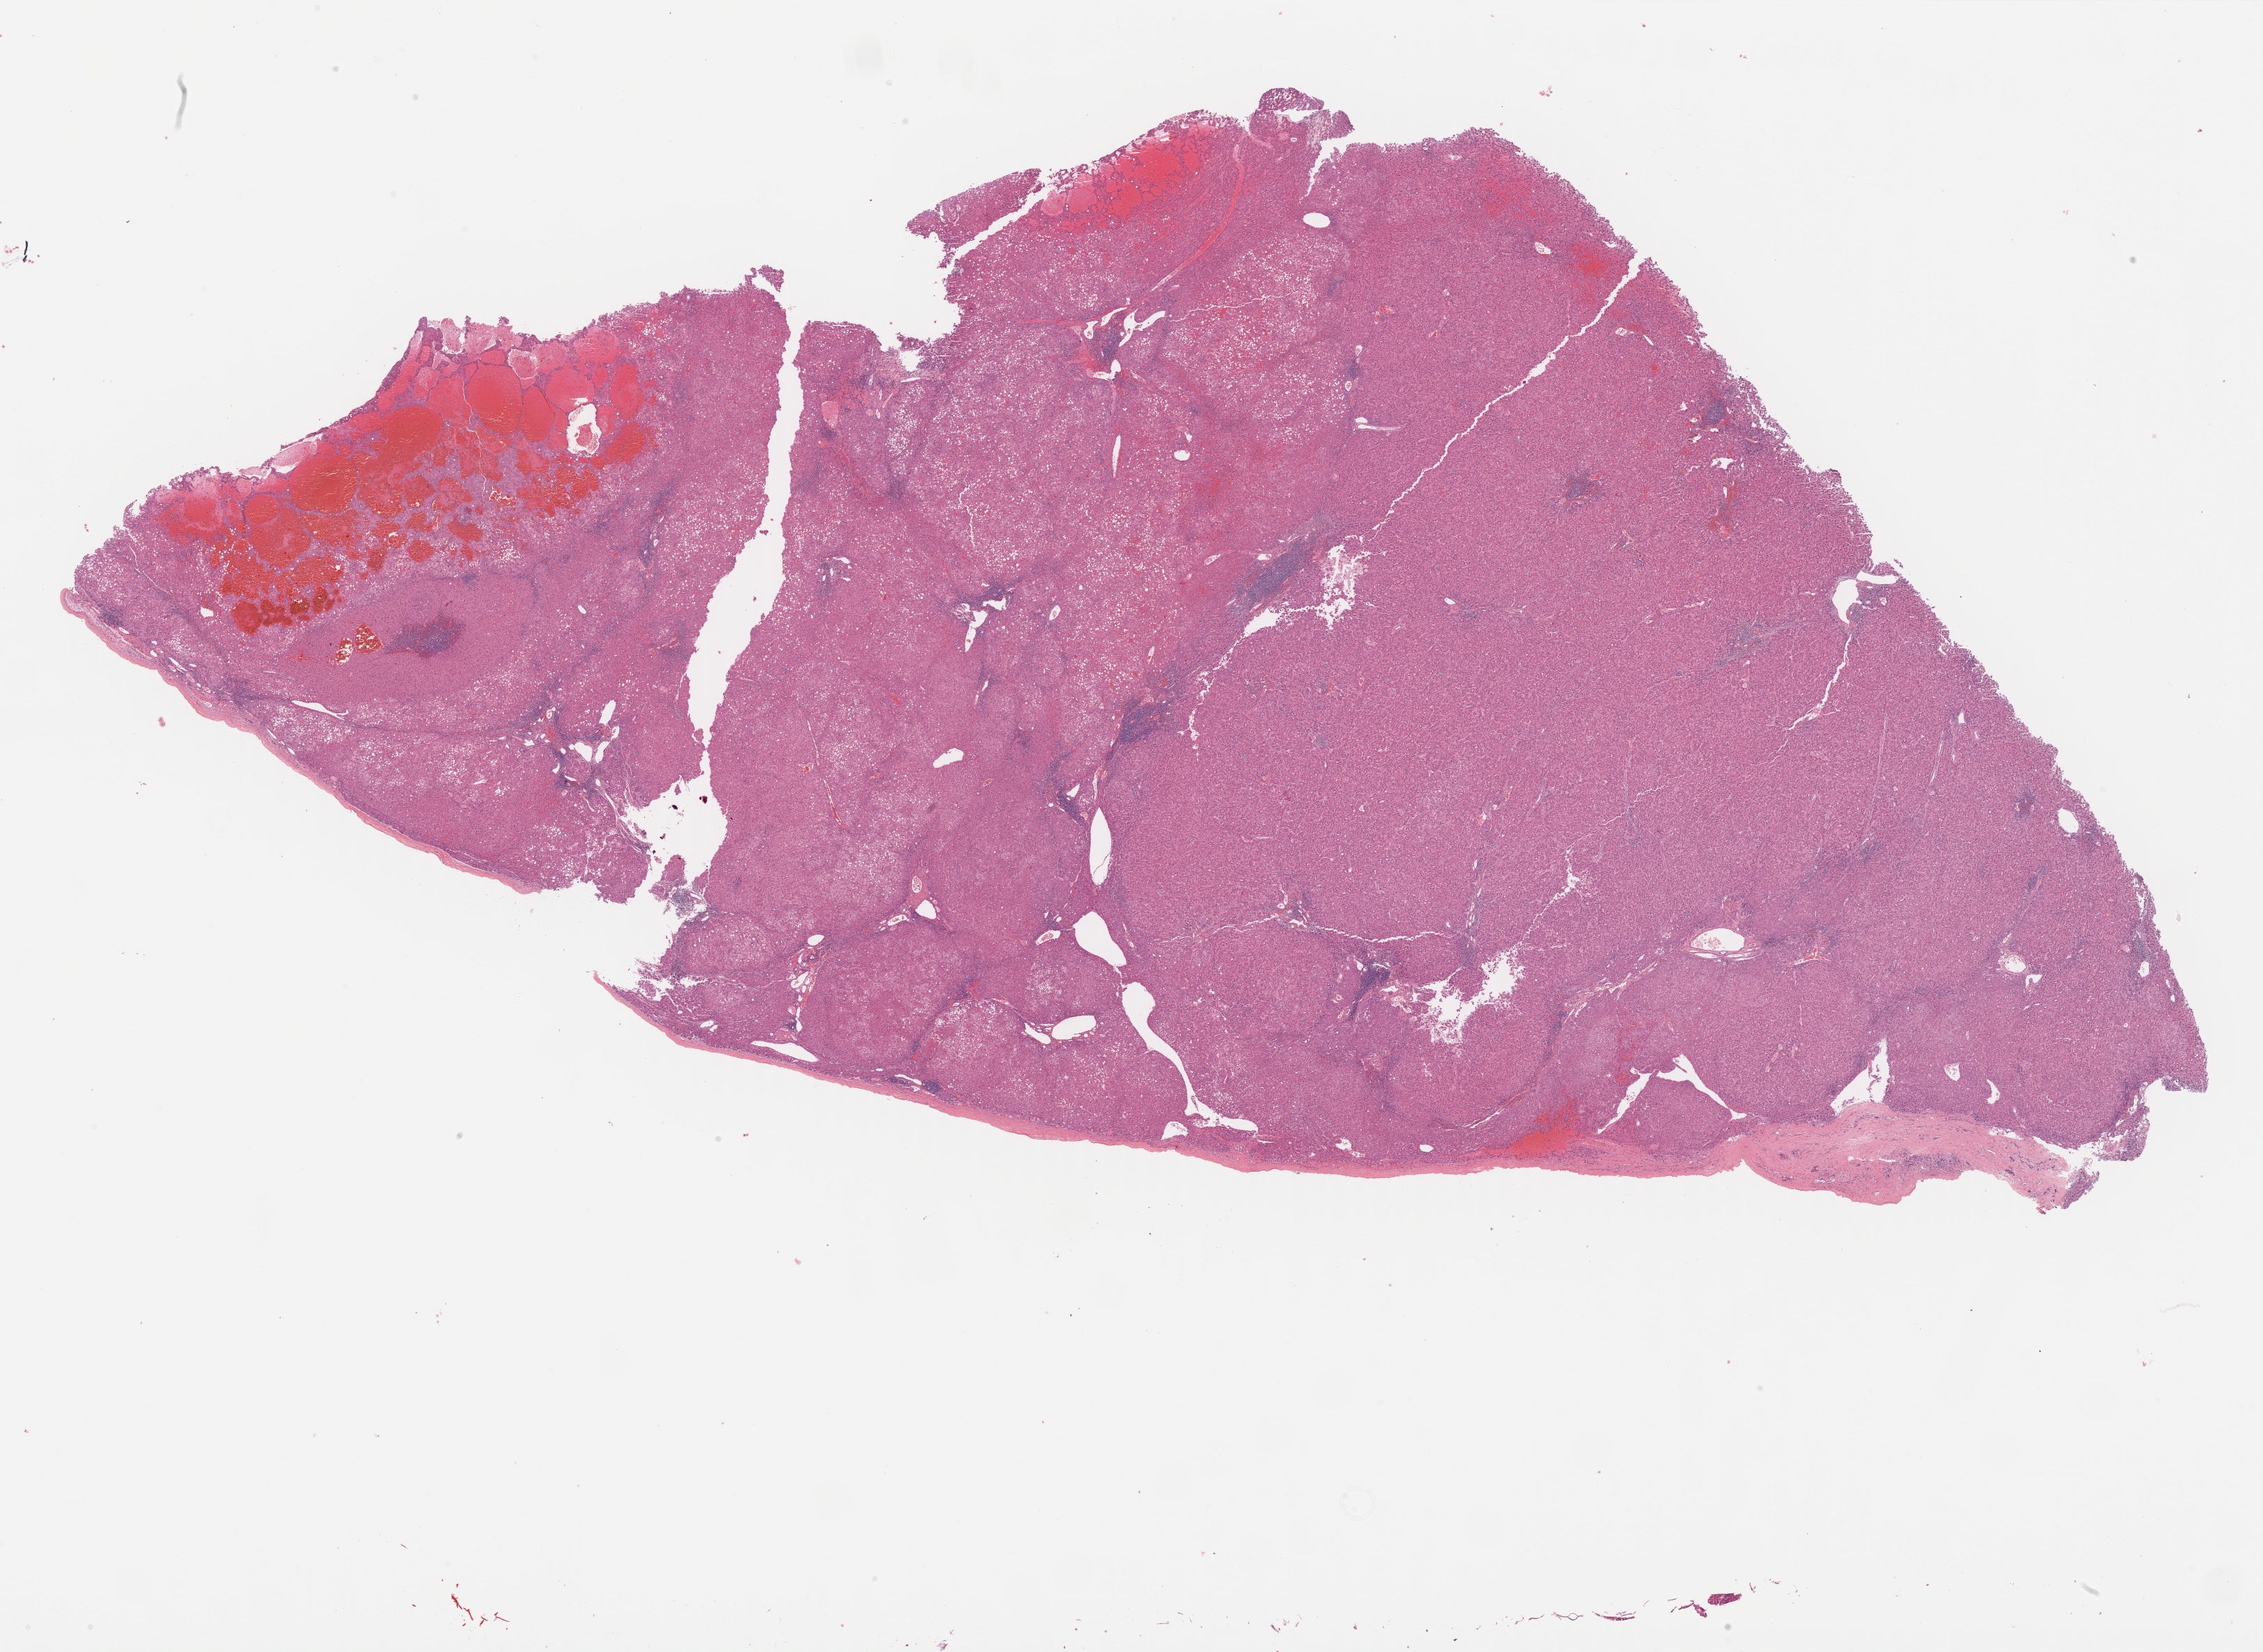
H&E whole-slide image, shown as a low-resolution overview of the whole scanned area (about 26.2 x 19.2 mm, acquisition: 40x scan). Formalin-fixed paraffin-embedded (FFPE) diagnostic section. Sample: primary tumour, liver. Patient: male, age at initial diagnosis 67 years.
Histologic diagnosis: Hepatocellular carcinoma, NOS.